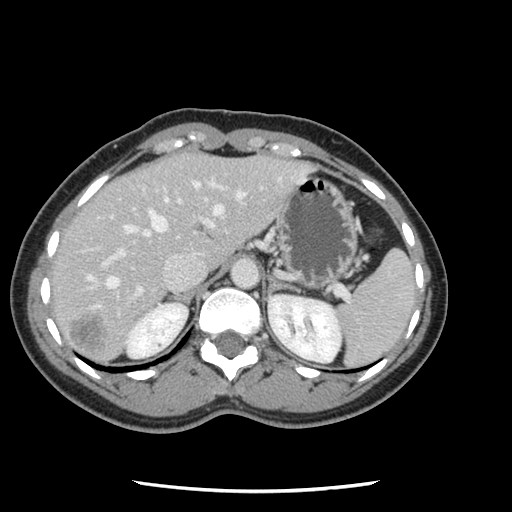
Contrast-enhanced abdominal CT, one axial slice. Slice 87 of 134 in the series (ordered by position). Intravenous contrast given. Soft-tissue window (W 400 / L 40 HU). 2.5 mm slice thickness. 512 × 512 image matrix, field of view 330 × 330 mm. Female patient, age 43 years. Case-level facts recorded for this patient, not image findings: diagnosis: colorectal cancer liver metastases, imaged before liver resection; multiple liver metastases: yes; largest metastasis: 3.4 cm; chemotherapy before resection: no.
Structures marked on this image (manually delineated by an expert):
- hepatic veins: box from (x=87, y=181) to (x=244, y=288) px
- liver: (x=51, y=153)–(x=309, y=363)
- planned liver remnant (the part of the liver to remain after resection): (x=51, y=157)–(x=191, y=309)
- portal vein (with intrahepatic branches): (x=84, y=180)–(x=224, y=315)
- liver metastasis: (x=71, y=317)–(x=105, y=350)